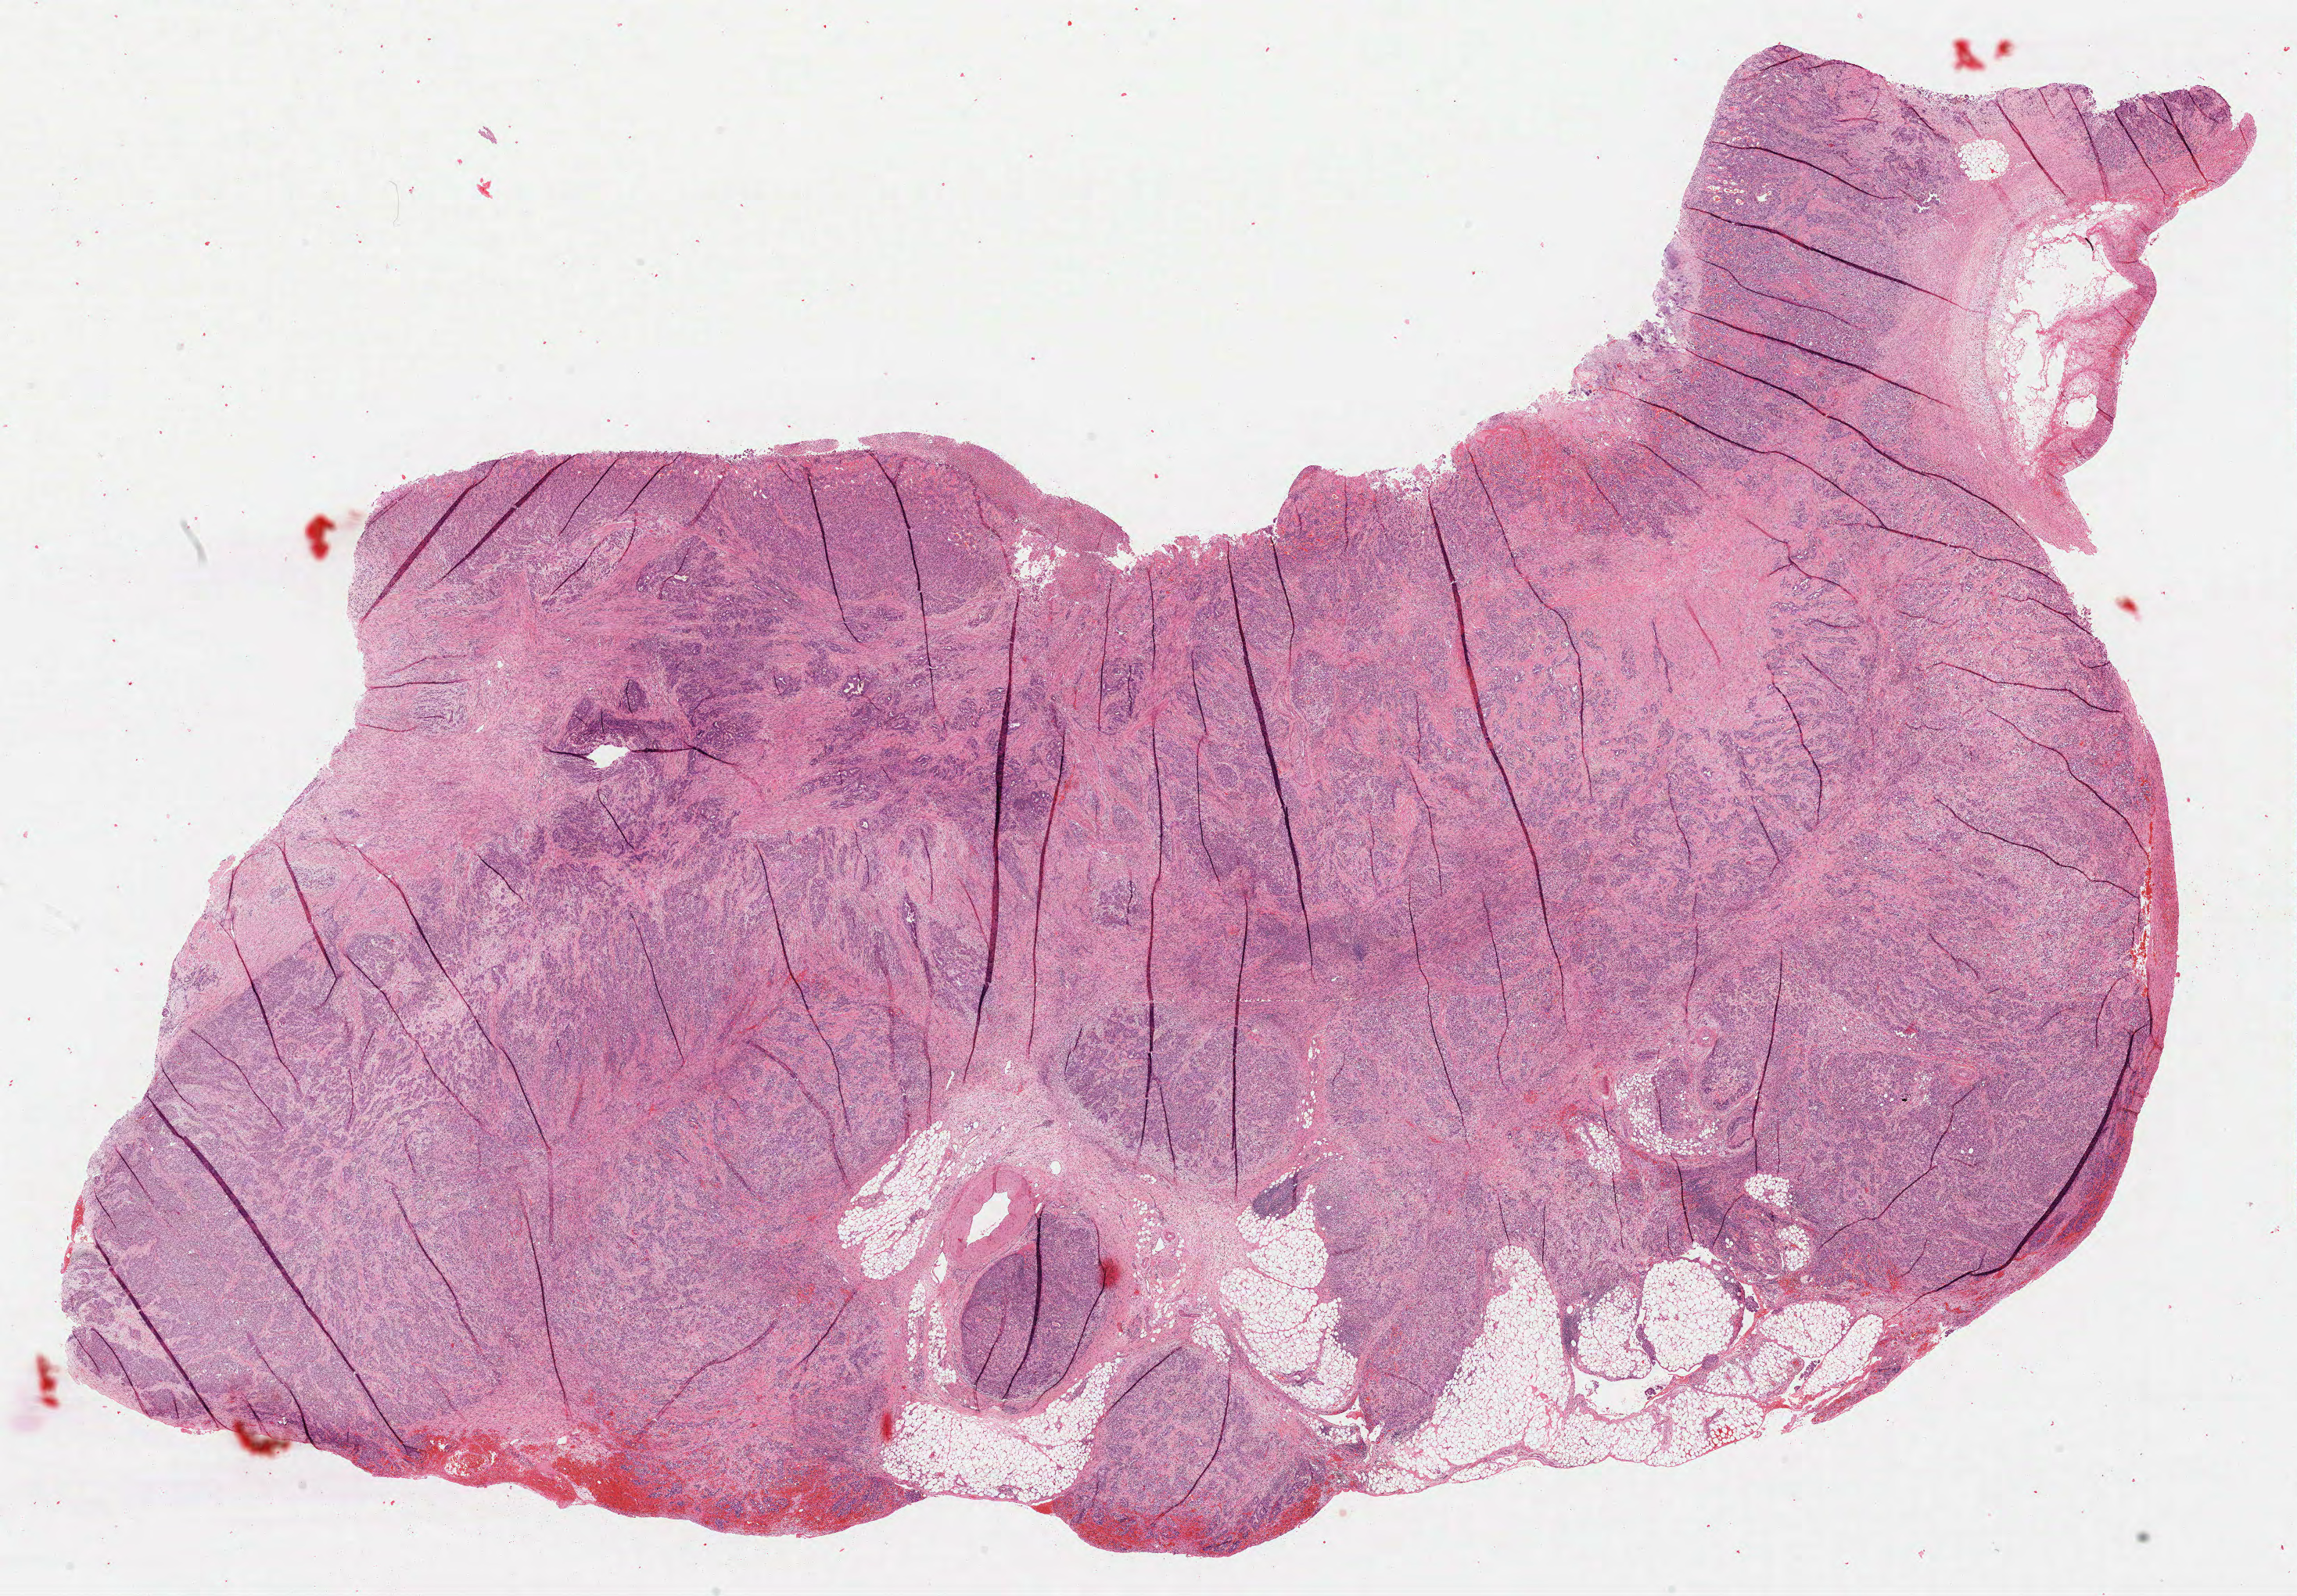
H&E whole-slide image, shown as a low-resolution overview of the whole scanned area (about 23.7 x 16.5 mm). FFPE section. Sample: primary tumour, stomach. Female, age 57 years at initial diagnosis. Histologic grade: G3 (poorly differentiated).
- pathologic diagnosis: Adenocarcinoma, NOS
- AJCC pathologic stage: IIB (7th edition)
- lymph nodes positive (case pathology): 1 of 15 examined